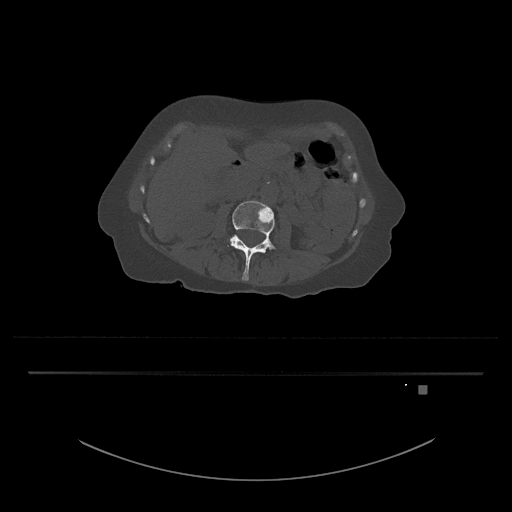
CT including the spine, one axial slice. Reconstruction kernel Br40s/3. 120 kVp. Bone window (W 1800 / L 400 HU). 0.5 mm slice thickness. 512 × 512 image matrix. Female patient, age 57 years. Case-level facts recorded for this patient, not image findings: primary cancer: cervical.
Annotated regions visible in this slice (semi-automatically segmented with operator editing):
- L3 vertebra: box from (x=226, y=200) to (x=276, y=281) px